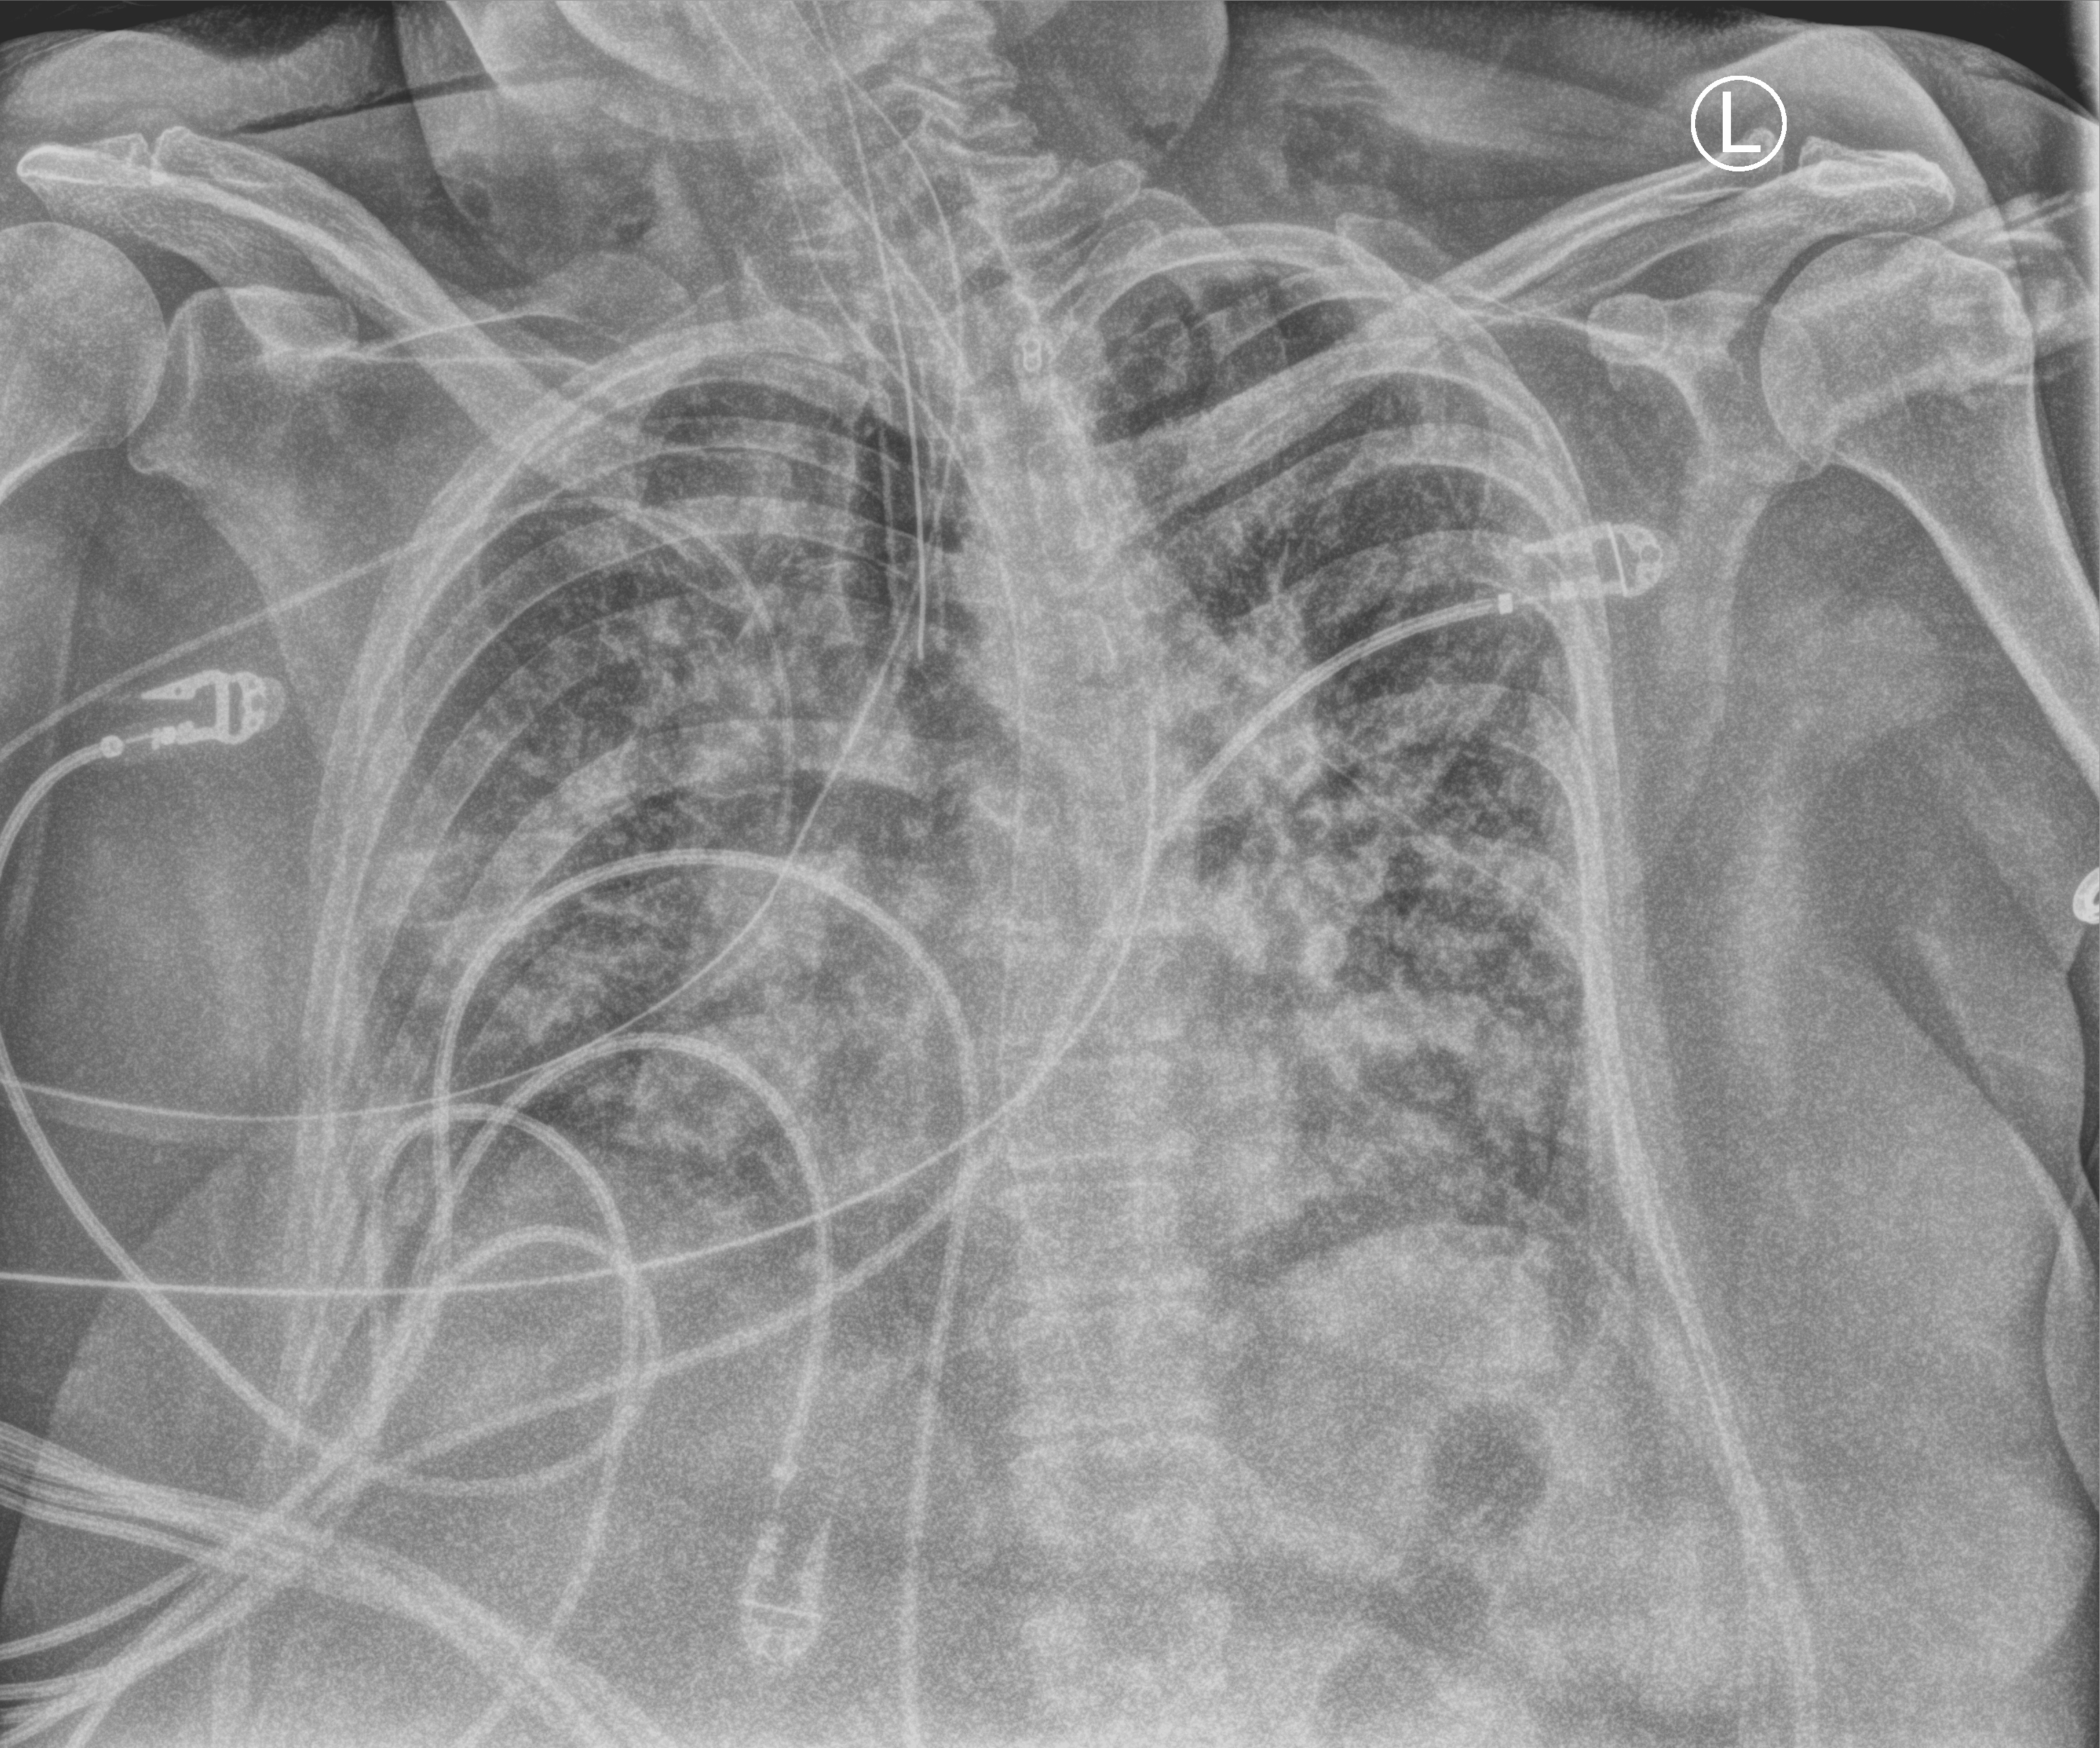
Portable chest radiograph, anteroposterior (AP) projection. Patient hospitalised with COVID-19; female, aged 60–74 years.
Admission-level facts for this patient (not findings on this image; timing relative to this image not recorded): COPD (admission record): no; mechanically ventilated during this hospital stay: yes.